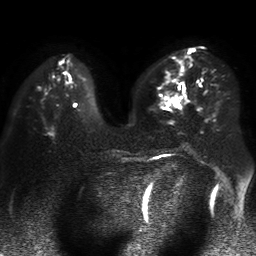
Breast MRI, one axial slice; position 22 of 50 along the scan axis; diffusion-weighted series; image 2 of 4 stored at this slice position (different b-values; order by instance number); 1.5 T; 256 × 256 image matrix. Female patient.
Structures marked on this image (manually delineated by an expert):
- tumour on diffusion-weighted imaging: bounding box (x1, y1, x2, y2) in pixels: (173, 100, 179, 105)